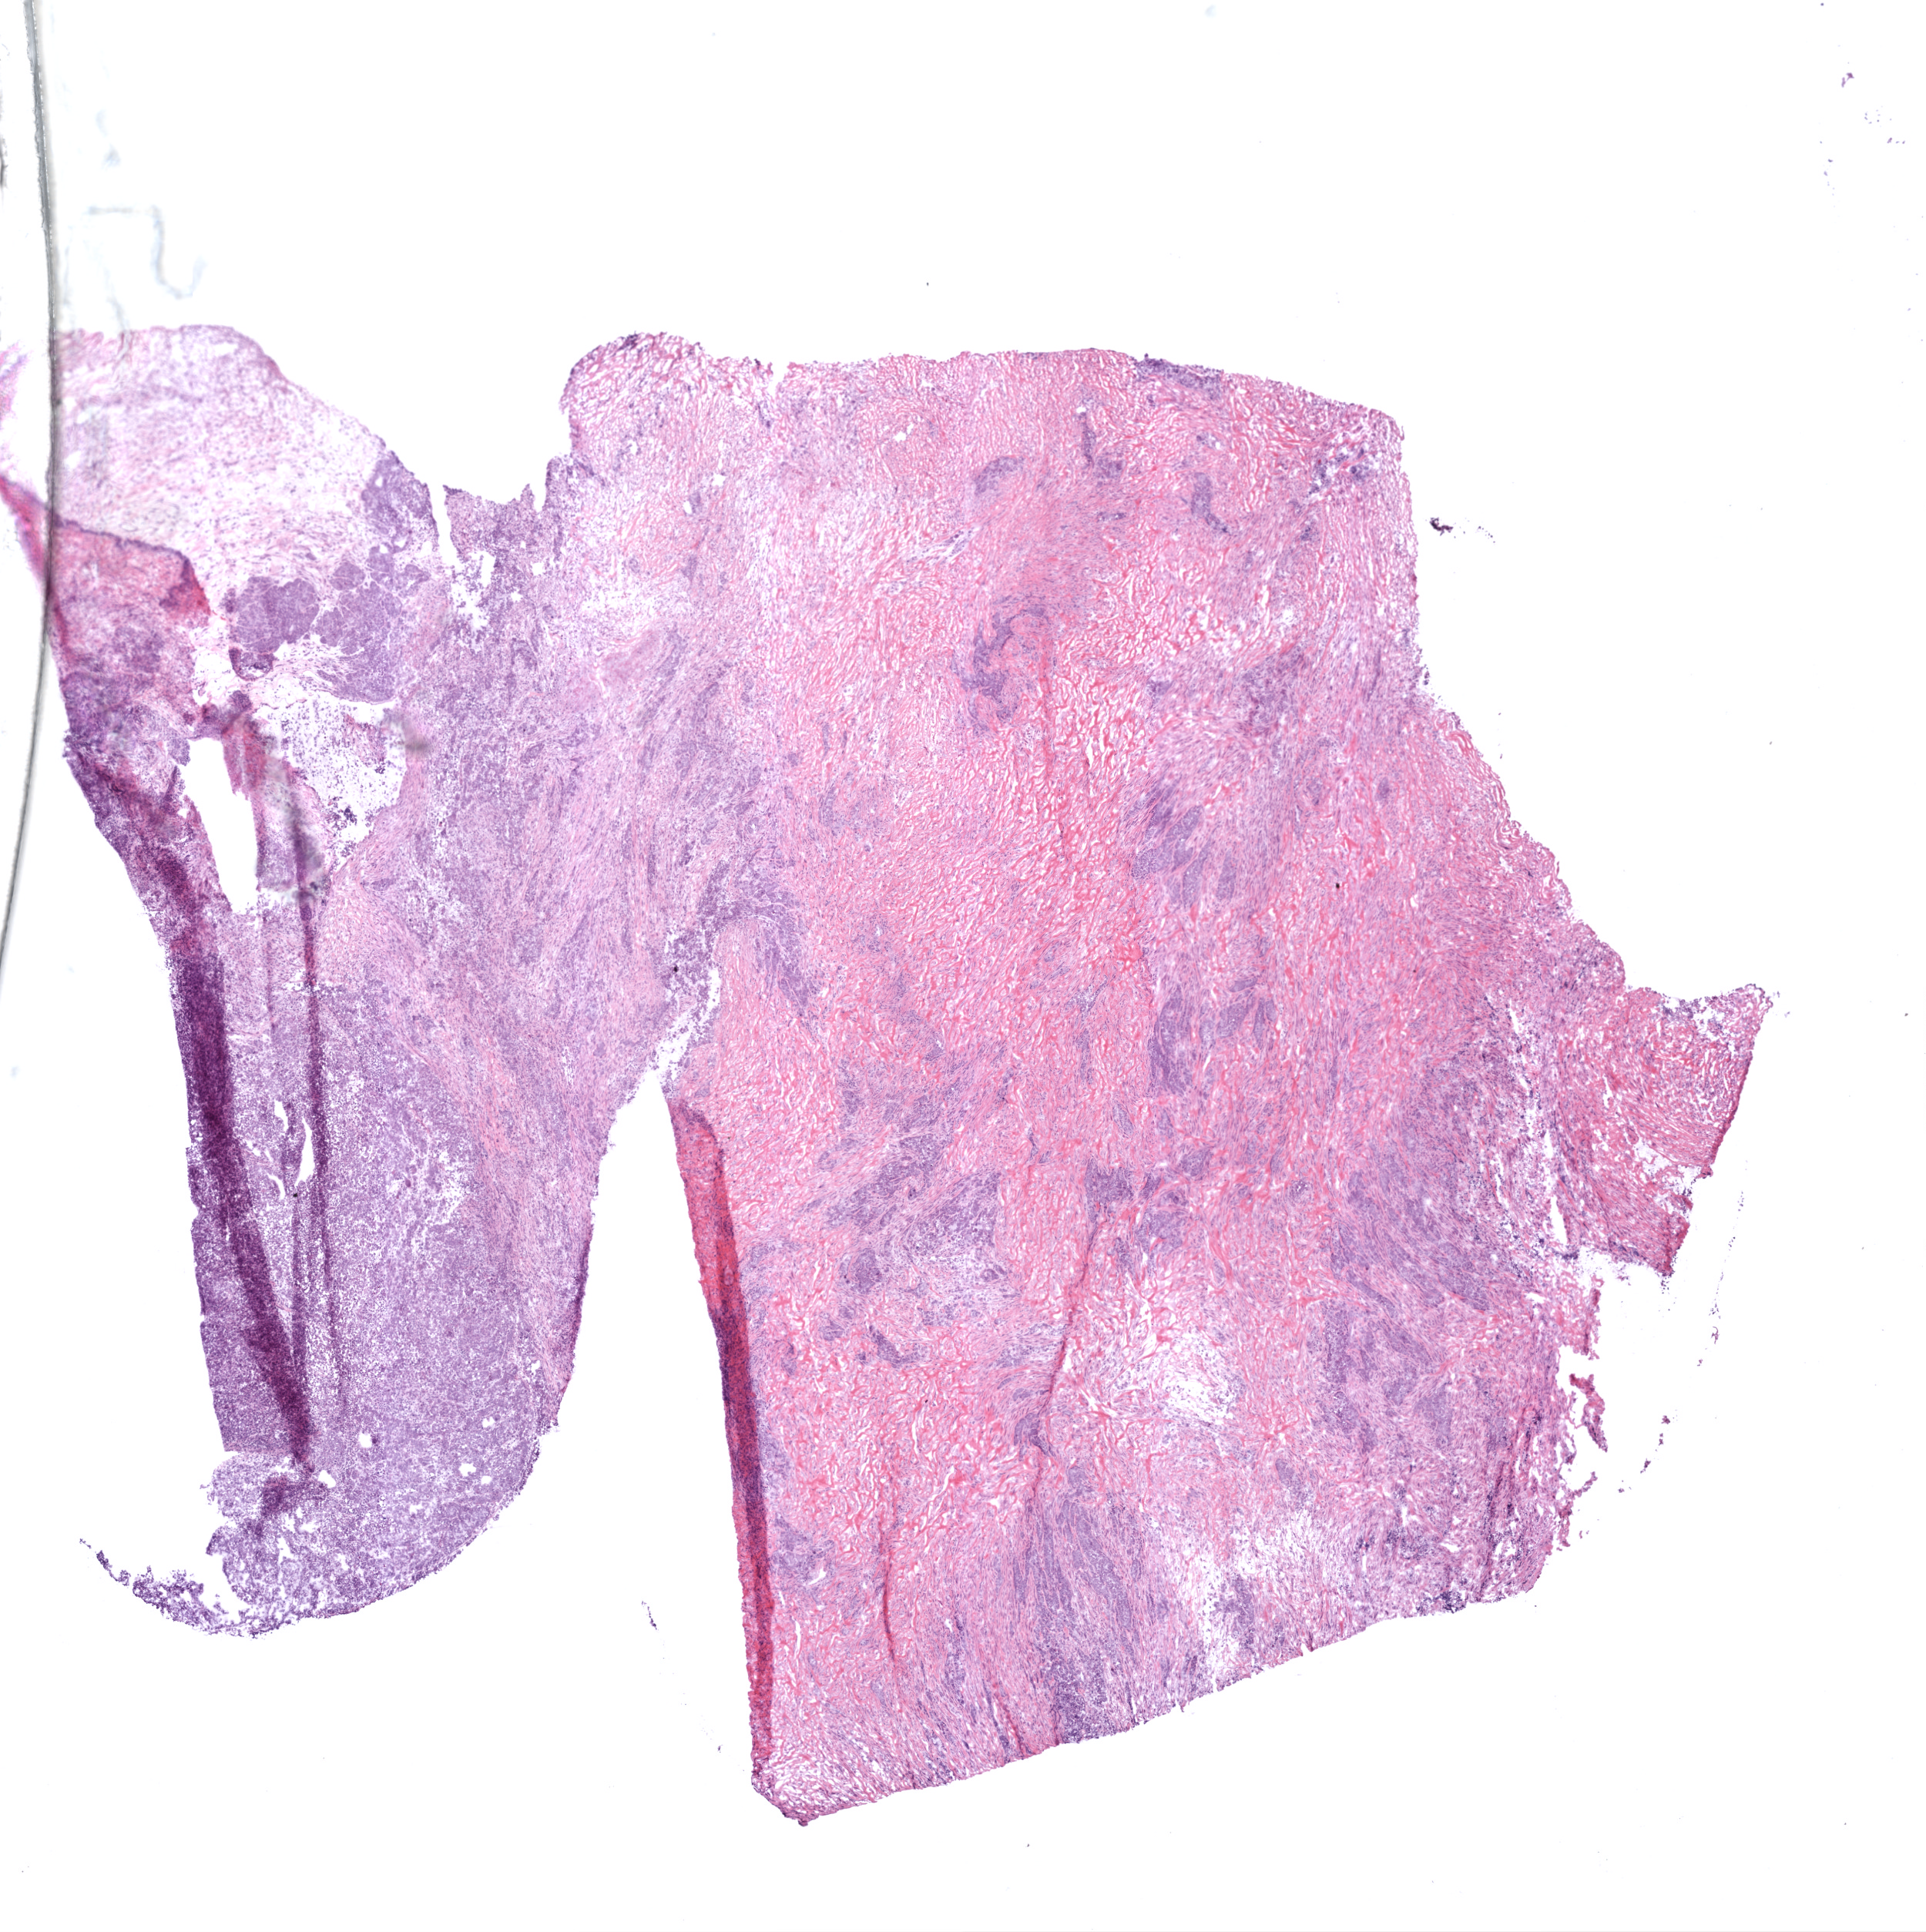
Whole-slide histology image, H&E — shown as a low-resolution overview of the whole scanned area (about 10.0 x 10.1 mm); frozen section; sample: primary tumour, ovary. Female patient; age at initial diagnosis 49 years. Histologic grade: G2 (moderately differentiated). Pathologist review of this section (percent, as recorded): tumour cells 60%, tumour nuclei 70%, normal cells 0%, stromal cells 40%, necrosis 0%. Inflammatory infiltration, as recorded: lymphocyte infiltration 2%.
FIGO stage: IV. Diagnosis: Serous cystadenocarcinoma, NOS.